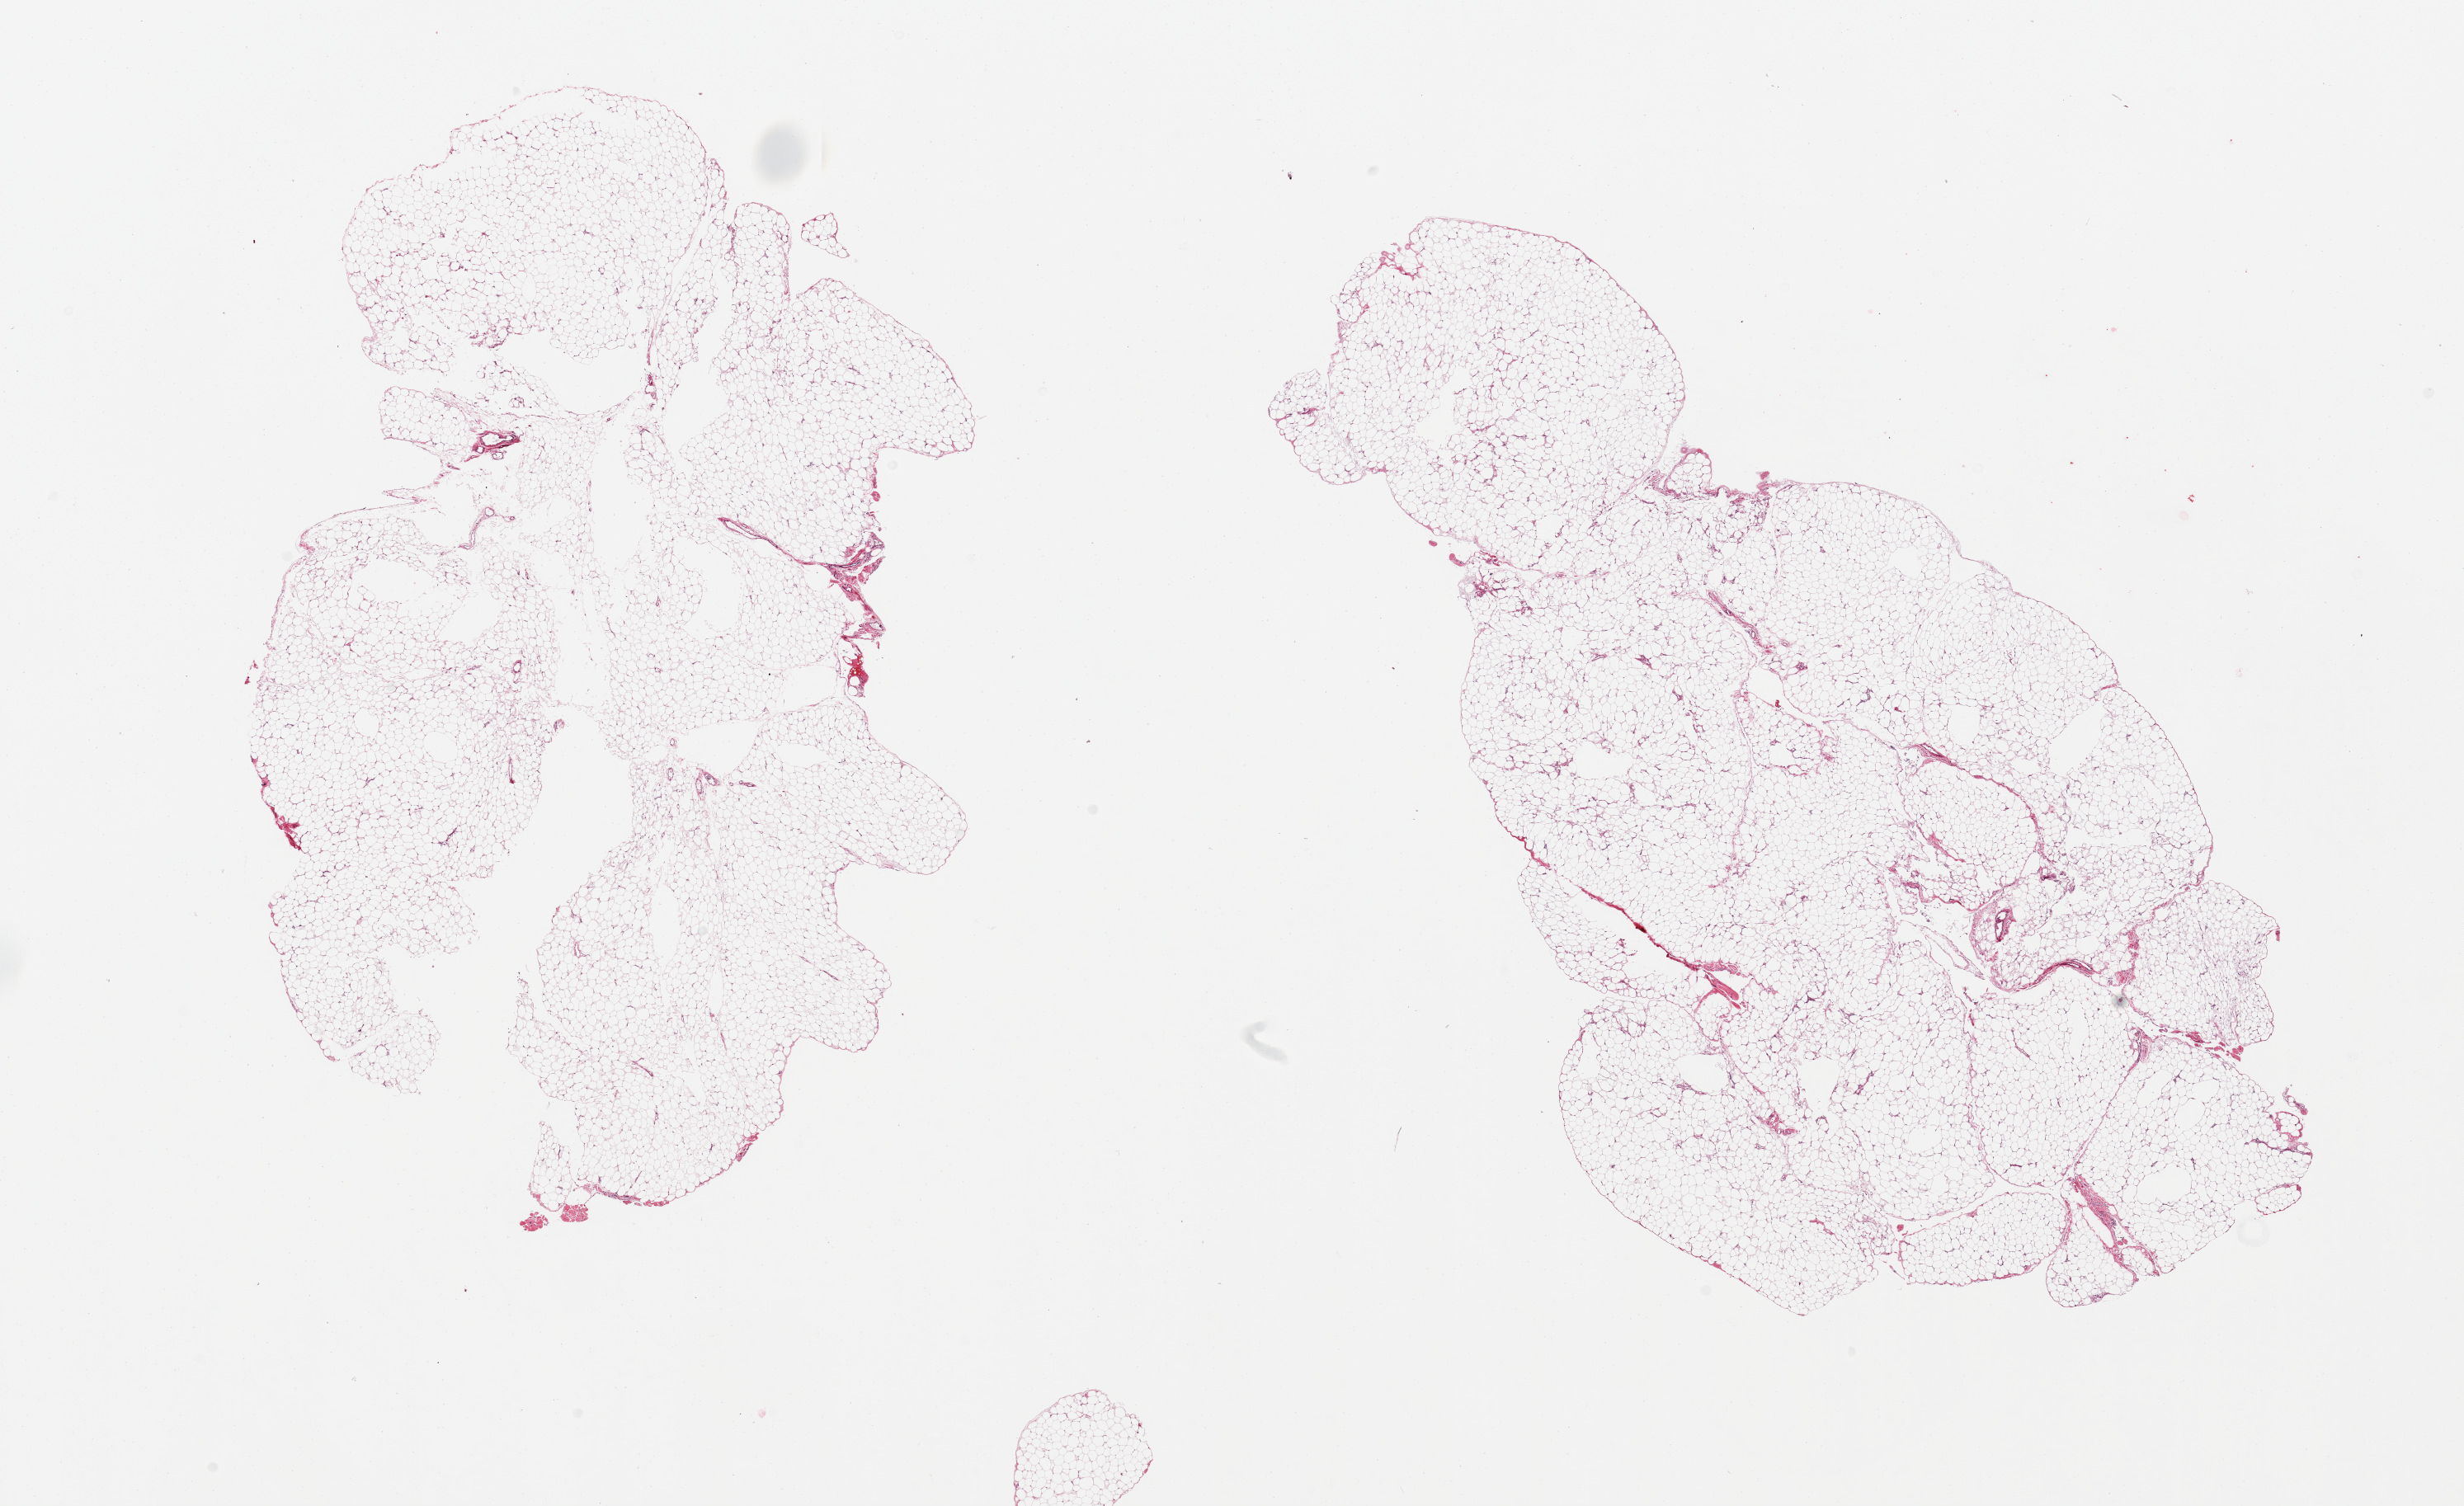
H&E whole-slide image — a low-resolution overview of the entire scanned area, about 23.6 x 14.4 mm; PAXgene-fixed paraffin-embedded (PFPE) section; section of omentum (target tissue); tissue donor sample.
Pathologist's review note for this sample: 2 pieces, minimal vascular / fascia elements.